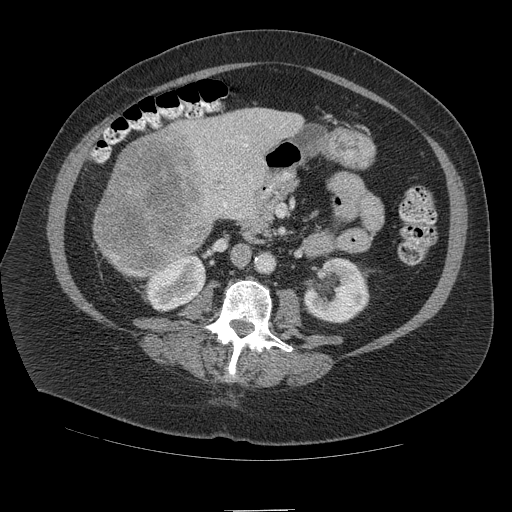
Contrast-enhanced abdominal CT (liver protocol), one axial slice. Slice 37 of 109 in the series (ordered by position). Reconstruction kernel STANDARD. 140 kVp. Soft-tissue window (W 400 / L 40 HU). 2.5 mm slice thickness. 512 × 512 image matrix. From the clinical record (not read from this slice): diagnosis: hepatocellular carcinoma (patient treated with transarterial chemoembolisation; whether this scan precedes or follows treatment is not stated here); TNM stage (as recorded): Stage-IVB; Child-Pugh class: A; tumour differentiation: poorly differentiated; tumour nodularity: multinodular.
Outlined on this slice (semi-automatically segmented with operator editing):
- liver parenchyma outside the tumour (the mass and vessels are separate outlines, so this box may not span the whole liver): bounding box [x1, y1, x2, y2] px = [94, 108, 302, 278]
- mass: [93, 126, 210, 277]
- liver vessels: [198, 136, 248, 208]